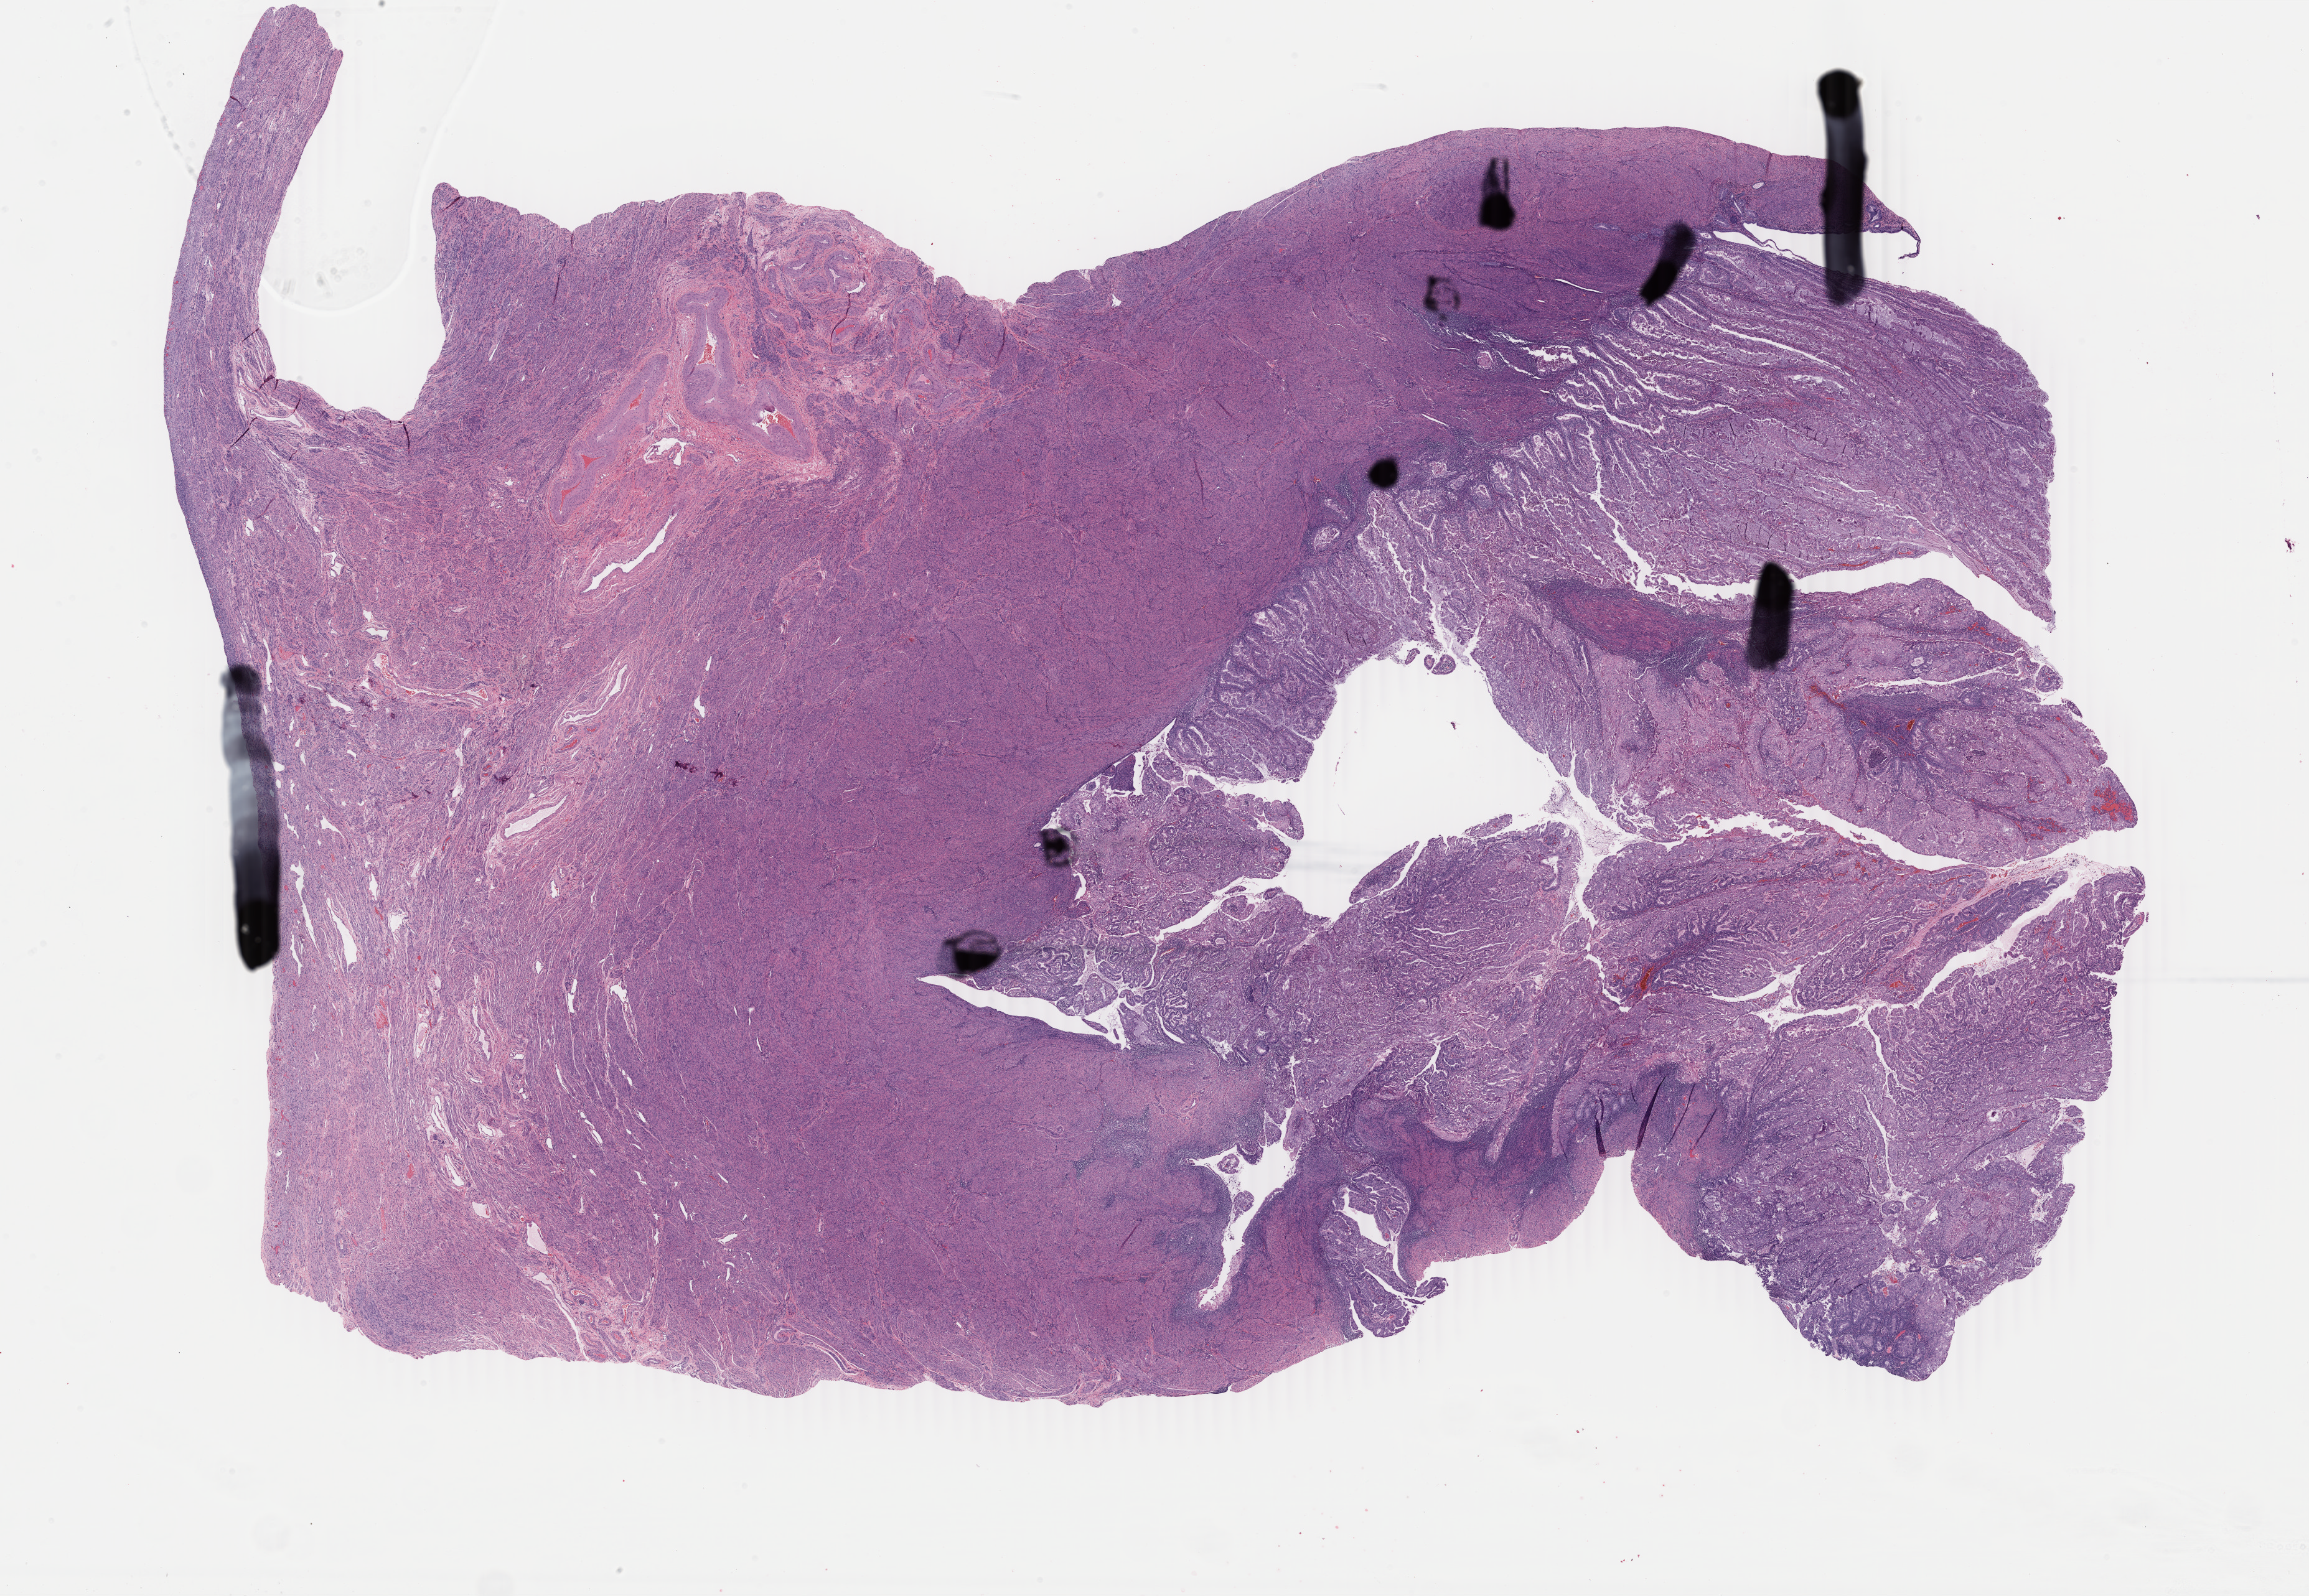
Whole-slide histology image, Hematoxylin and eosin (H&E) stained — low-resolution overview of the scanned area, about 29.5 x 20.4 mm. Formalin-fixed paraffin-embedded (FFPE) diagnostic section. Primary tumour sample from the uterus. Female, age 58 years at initial diagnosis. Histologic grade: G1 (well differentiated).
FIGO stage: IIIA. Histologic diagnosis: Endometrioid adenocarcinoma, NOS (endometrium).